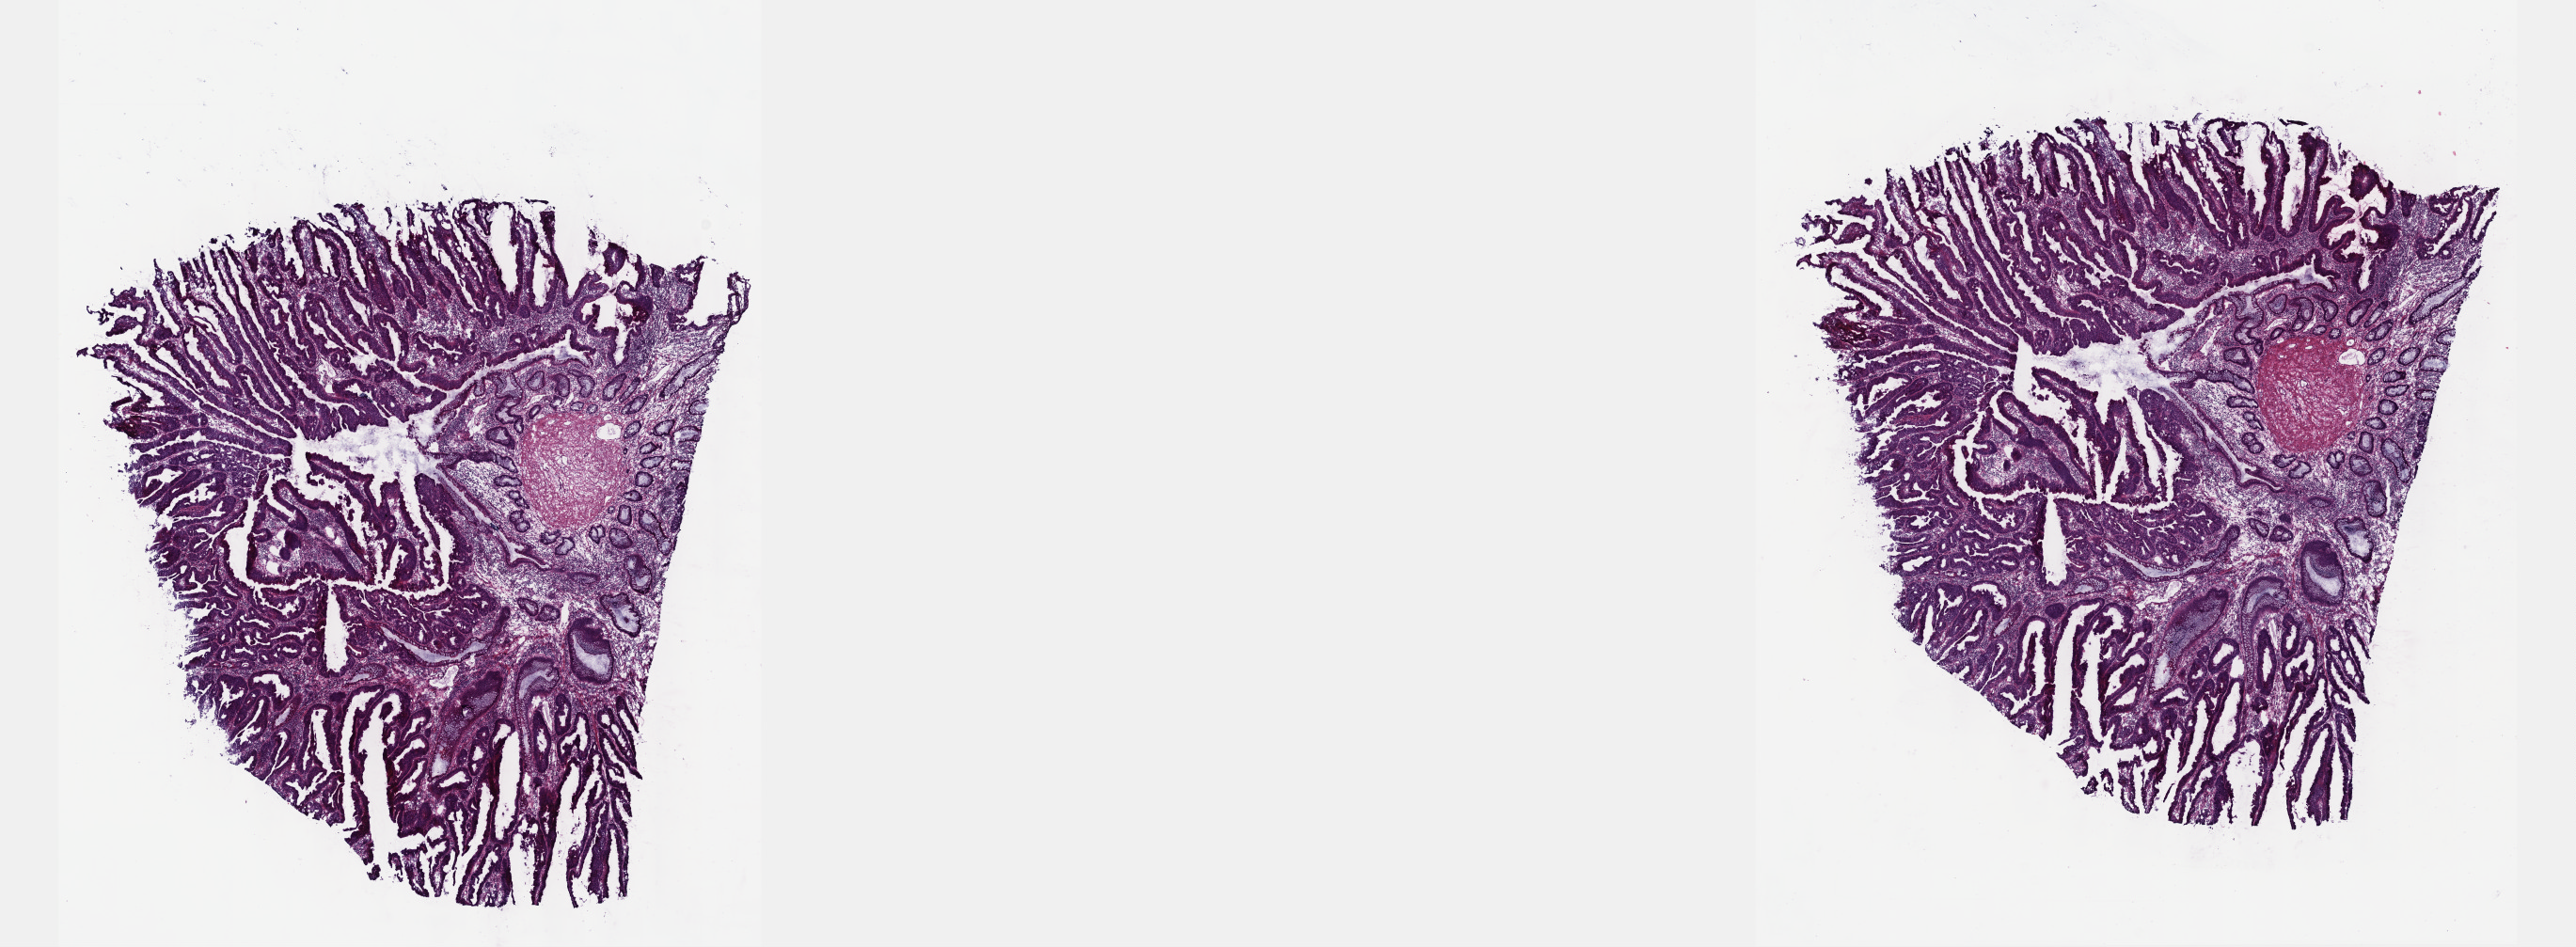
Whole-slide histology image, H&E — low-resolution overview of the scanned area, about 22.1 x 8.1 mm; frozen section from the top of the tissue portion; colon, primary tumour sample. Female, age 42 years at initial diagnosis. Slide review estimates, as recorded: tumour cells 60%, tumour nuclei 60%, normal cells 25%, stromal cells 15%, necrosis 0%. Inflammatory infiltration, as recorded: lymphocyte infiltration 5%, monocyte infiltration 2%, neutrophil infiltration 2%.
- TNM: T3 N0 MX
- lymph nodes positive (case pathology): 0 of 24 examined
- AJCC pathologic stage: IIA (7th edition)
- diagnosis: Mucinous adenocarcinoma (descending colon)